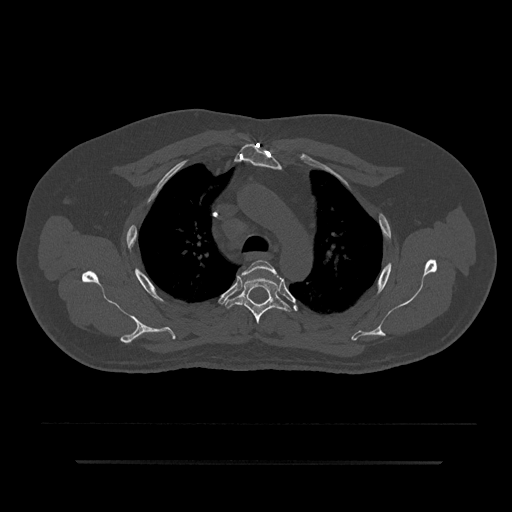
CT including the spine, one axial slice; position 624 of 797 along the scan axis; reconstruction kernel Br40s/3; 120 kVp; bone window (W 1800 / L 400 HU); 512 × 512 image matrix, field of view 464 × 464 mm. Male patient, age 59 years. Case-level facts recorded for this patient, not image findings: primary cancer: bile ducts.
Outlined on this slice (semi-automatically segmented with operator editing):
- T3 vertebra: box from (x=242, y=260) to (x=282, y=283) px
- T4 vertebra: (x=224, y=272)–(x=291, y=324)